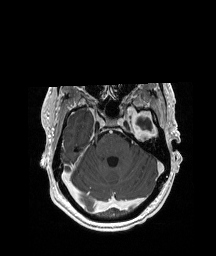
Brain MRI from a brain-tumour surgery series, one axial slice. Position 140 of 208 along the scan axis. T1-weighted post-contrast. 1 mm slice thickness. 216 × 256 image matrix, field of view 228 × 270 mm. Case-level facts recorded for this patient, not image findings: histopathology: Glioblastoma; WHO grade: 4; IDH mutation: no; tumour location: Left Anterior/Superior Temporal.
Annotated regions visible in this slice (outlined manually by an expert reader):
- previous resection cavity: box from (x=136, y=117) to (x=153, y=131) px
- tumour: (x=123, y=102)–(x=158, y=136)